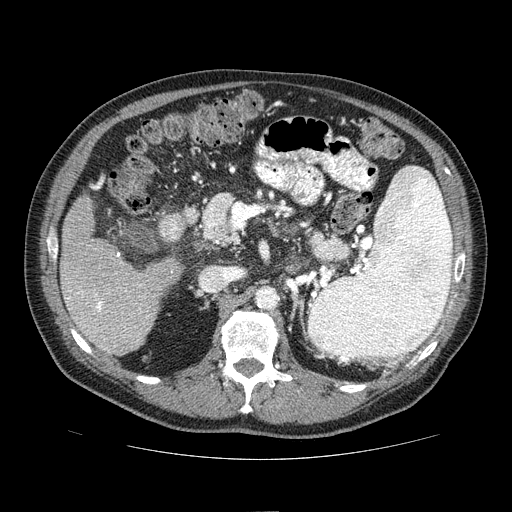
Contrast-enhanced abdominal CT (liver protocol), one axial slice. Position 29 of 81 along the scan axis. Reconstruction kernel STANDARD. 100 kVp. One of 2 acquisitions stored at this slice position. Soft-tissue window (W 400 / L 40 HU). 2.5 mm slice thickness. 512 × 512 image matrix, field of view 400 × 400 mm. Case-level facts recorded for this patient, not image findings: diagnosis: hepatocellular carcinoma (patient treated with transarterial chemoembolisation; whether this scan precedes or follows treatment is not stated here); TNM stage (as recorded): Stage-IIIA; Child-Pugh class: A; tumour differentiation: well differentiated; tumour nodularity: multinodular.
Annotated regions visible in this slice (semi-automatically segmented with operator editing):
- liver parenchyma outside the tumour (the mass and vessels are separate outlines, so this box may not span the whole liver): box from (x=60, y=196) to (x=182, y=355) px
- liver vessels: (x=66, y=253)–(x=148, y=341)